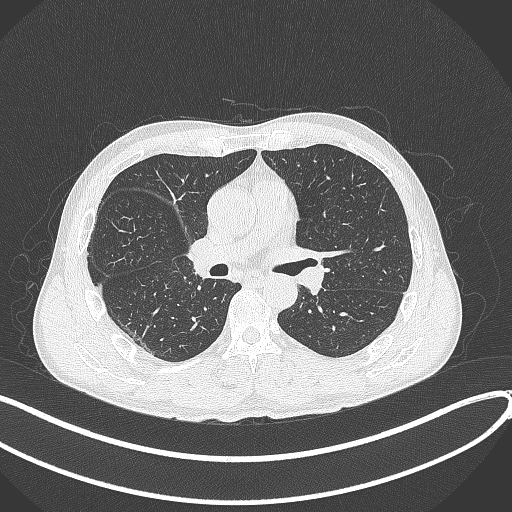
Chest CT, one axial slice; position 218 of 409 along the scan axis; reconstruction kernel B70f; lung window (W 1500 / L -600 HU); 1 mm slice thickness; 512 × 512 image matrix, field of view 400 × 400 mm. Patient: male, 53 years. Case-level facts recorded for this patient, not image findings: clinical TNM (as recorded): T1b N0 M0.
Structures marked on this image (bounding box drawn by a radiologist):
- lung tumour (recorded histology: squamous cell carcinoma): bounding box (x1, y1, x2, y2) in pixels: (186, 233, 220, 278)